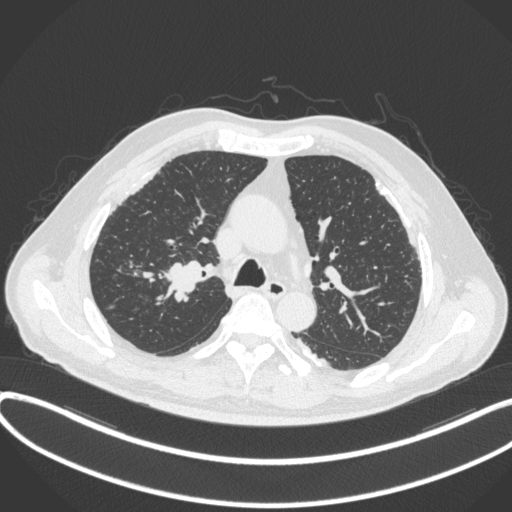
Chest CT, one axial slice. Position 288 of 455 along the scan axis. Reconstruction kernel B31f. 120 kVp. Lung window (W 1500 / L -600 HU). 1 mm slice thickness. 512 × 512 image matrix, field of view 400 × 400 mm. Male patient, age 58 years. Case-level facts recorded for this patient, not image findings: clinical TNM (as recorded): T1c N0 M0.
Annotated regions visible in this slice (bounding box drawn by a radiologist):
- lung tumour (recorded histology: squamous cell carcinoma): bounding box [x1, y1, x2, y2] px = [159, 255, 205, 302]